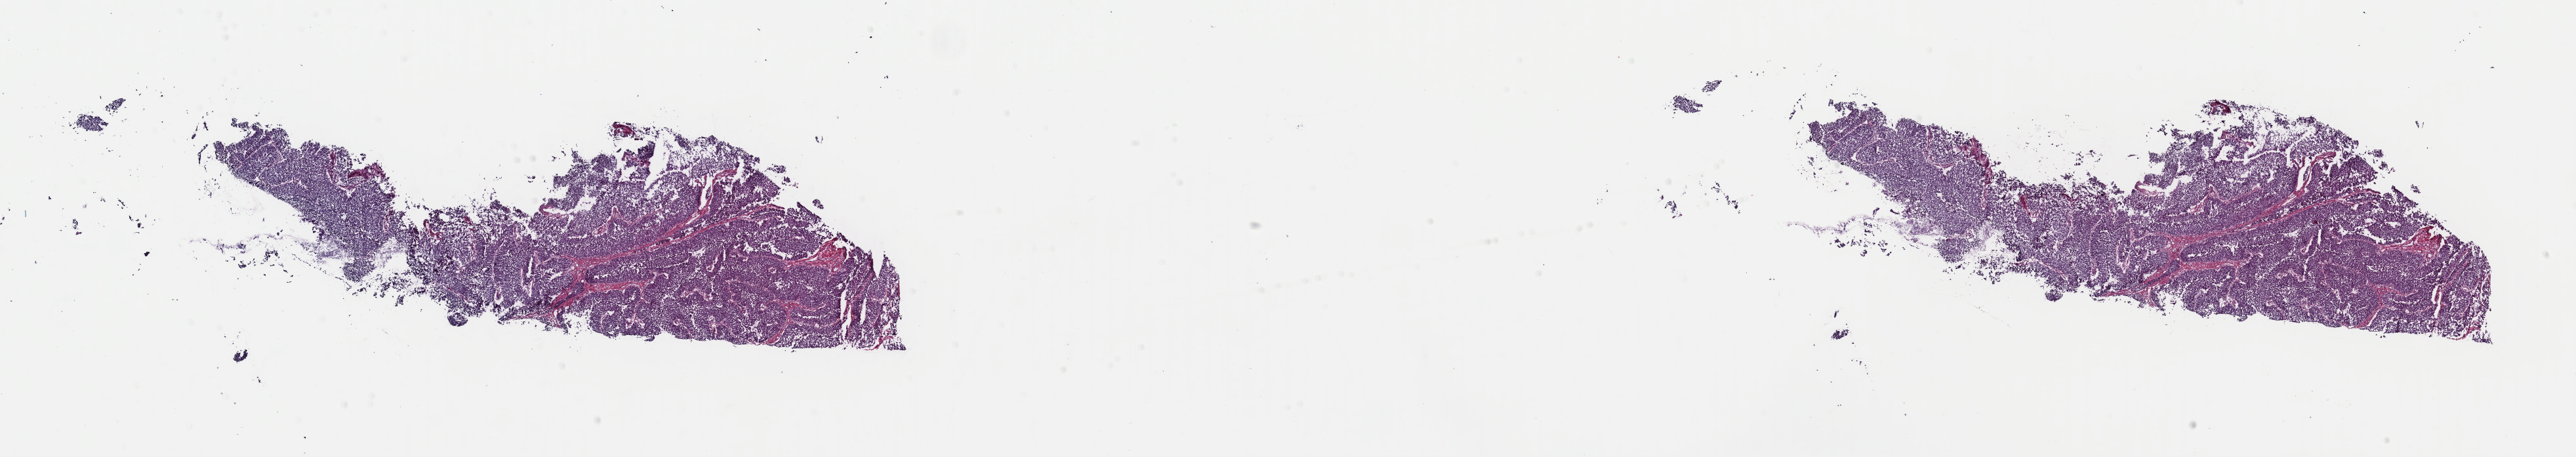
Digitized Hematoxylin and eosin (H&E) stained tissue section (whole slide), shown as a low-resolution overview of the whole scanned area (about 31.0 x 5.5 mm, acquisition: 40x scan). Frozen section from the top of the tissue portion. Bladder, primary tumour sample. Patient: male, age at initial diagnosis 84 years. Histologic grade: high grade. Slide review estimates, as recorded: tumour cells 100%, tumour nuclei 80%, normal cells 0%, stromal cells 0%, necrosis 0%. Inflammatory infiltration, as recorded: lymphocyte infiltration 1%, monocyte infiltration 0%, neutrophil infiltration 0%.
- pathologic diagnosis: Papillary transitional cell carcinoma (posterior wall of bladder)
- AJCC pathologic stage: II